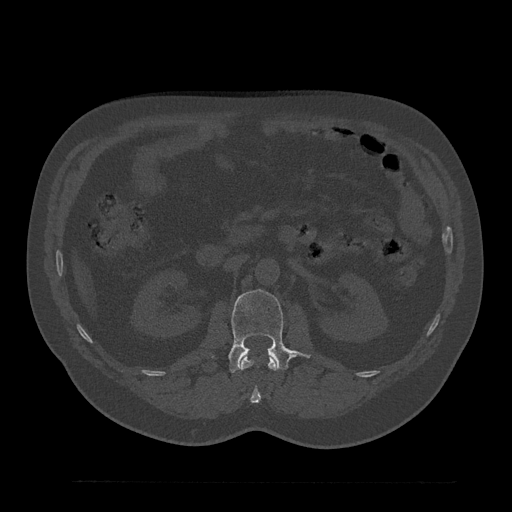
CT including the spine, one axial slice. Position 118 of 797 along the scan axis. Reconstruction kernel Br40s/3. 120 kVp. Bone window (W 1800 / L 400 HU). 0.5 mm slice thickness. 512 × 512 image matrix, field of view 430 × 430 mm. Male patient, age 61 years. Case-level facts recorded for this patient, not image findings: primary cancer: prostate.
Structures marked on this image (semi-automatic segmentation, software-assisted and operator-edited):
- L1 vertebra: bounding box [x1, y1, x2, y2] px = [241, 354, 278, 403]
- L2 vertebra: [229, 289, 309, 373]